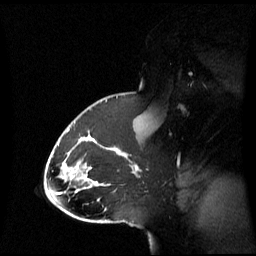
Breast MRI (dynamic contrast-enhanced), one sagittal slice. Dynamic contrast-enhanced series, image 2 of 3 at this slice position (ordered by acquisition). 1.5 T. TE 4.2 ms, TR 8.4 ms. 2.8 mm slice thickness. 256 × 256 image matrix. Female patient, age 43 years. From the clinical record (not read from this slice): setting: breast cancer imaged before/during neoadjuvant chemotherapy; receptor status: triple-negative.
Annotated regions visible in this slice (semi-automatically segmented with operator editing):
- analysis volume of interest (the breast-tissue region the enhancement analysis was run in; not a lesion): box from (x=65, y=118) to (x=143, y=197) px
- tumour enhancement mask (voxels above the 70 % enhancement threshold inside the analysis volume of interest): (x=68, y=129)–(x=137, y=169)